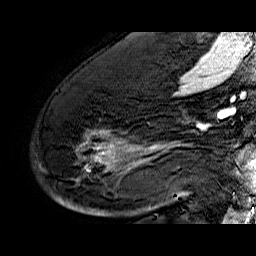
Breast MRI (dynamic contrast-enhanced), one sagittal slice. Slice 39 of 60 in the series (ordered by position). Dynamic contrast-enhanced series, time point 2 of 6 at this slice position (early post-contrast). 1.5 T. TE 6.4 ms, TR 32.9 ms. 4 mm slice thickness. 256 × 256 image matrix. Female patient. Case-level facts recorded for this patient, not image findings: setting: breast cancer imaged before/during neoadjuvant chemotherapy; receptor status: HR-positive, HER2-negative.
Structures marked on this image (semi-automatic segmentation, software-assisted and operator-edited):
- analysis volume of interest (the breast-tissue region the enhancement analysis was run in; not a lesion): bounding box [x1, y1, x2, y2] px = [50, 74, 176, 210]
- tumour enhancement mask (voxels above the 100 % enhancement threshold inside the analysis volume of interest): [59, 130, 176, 200]